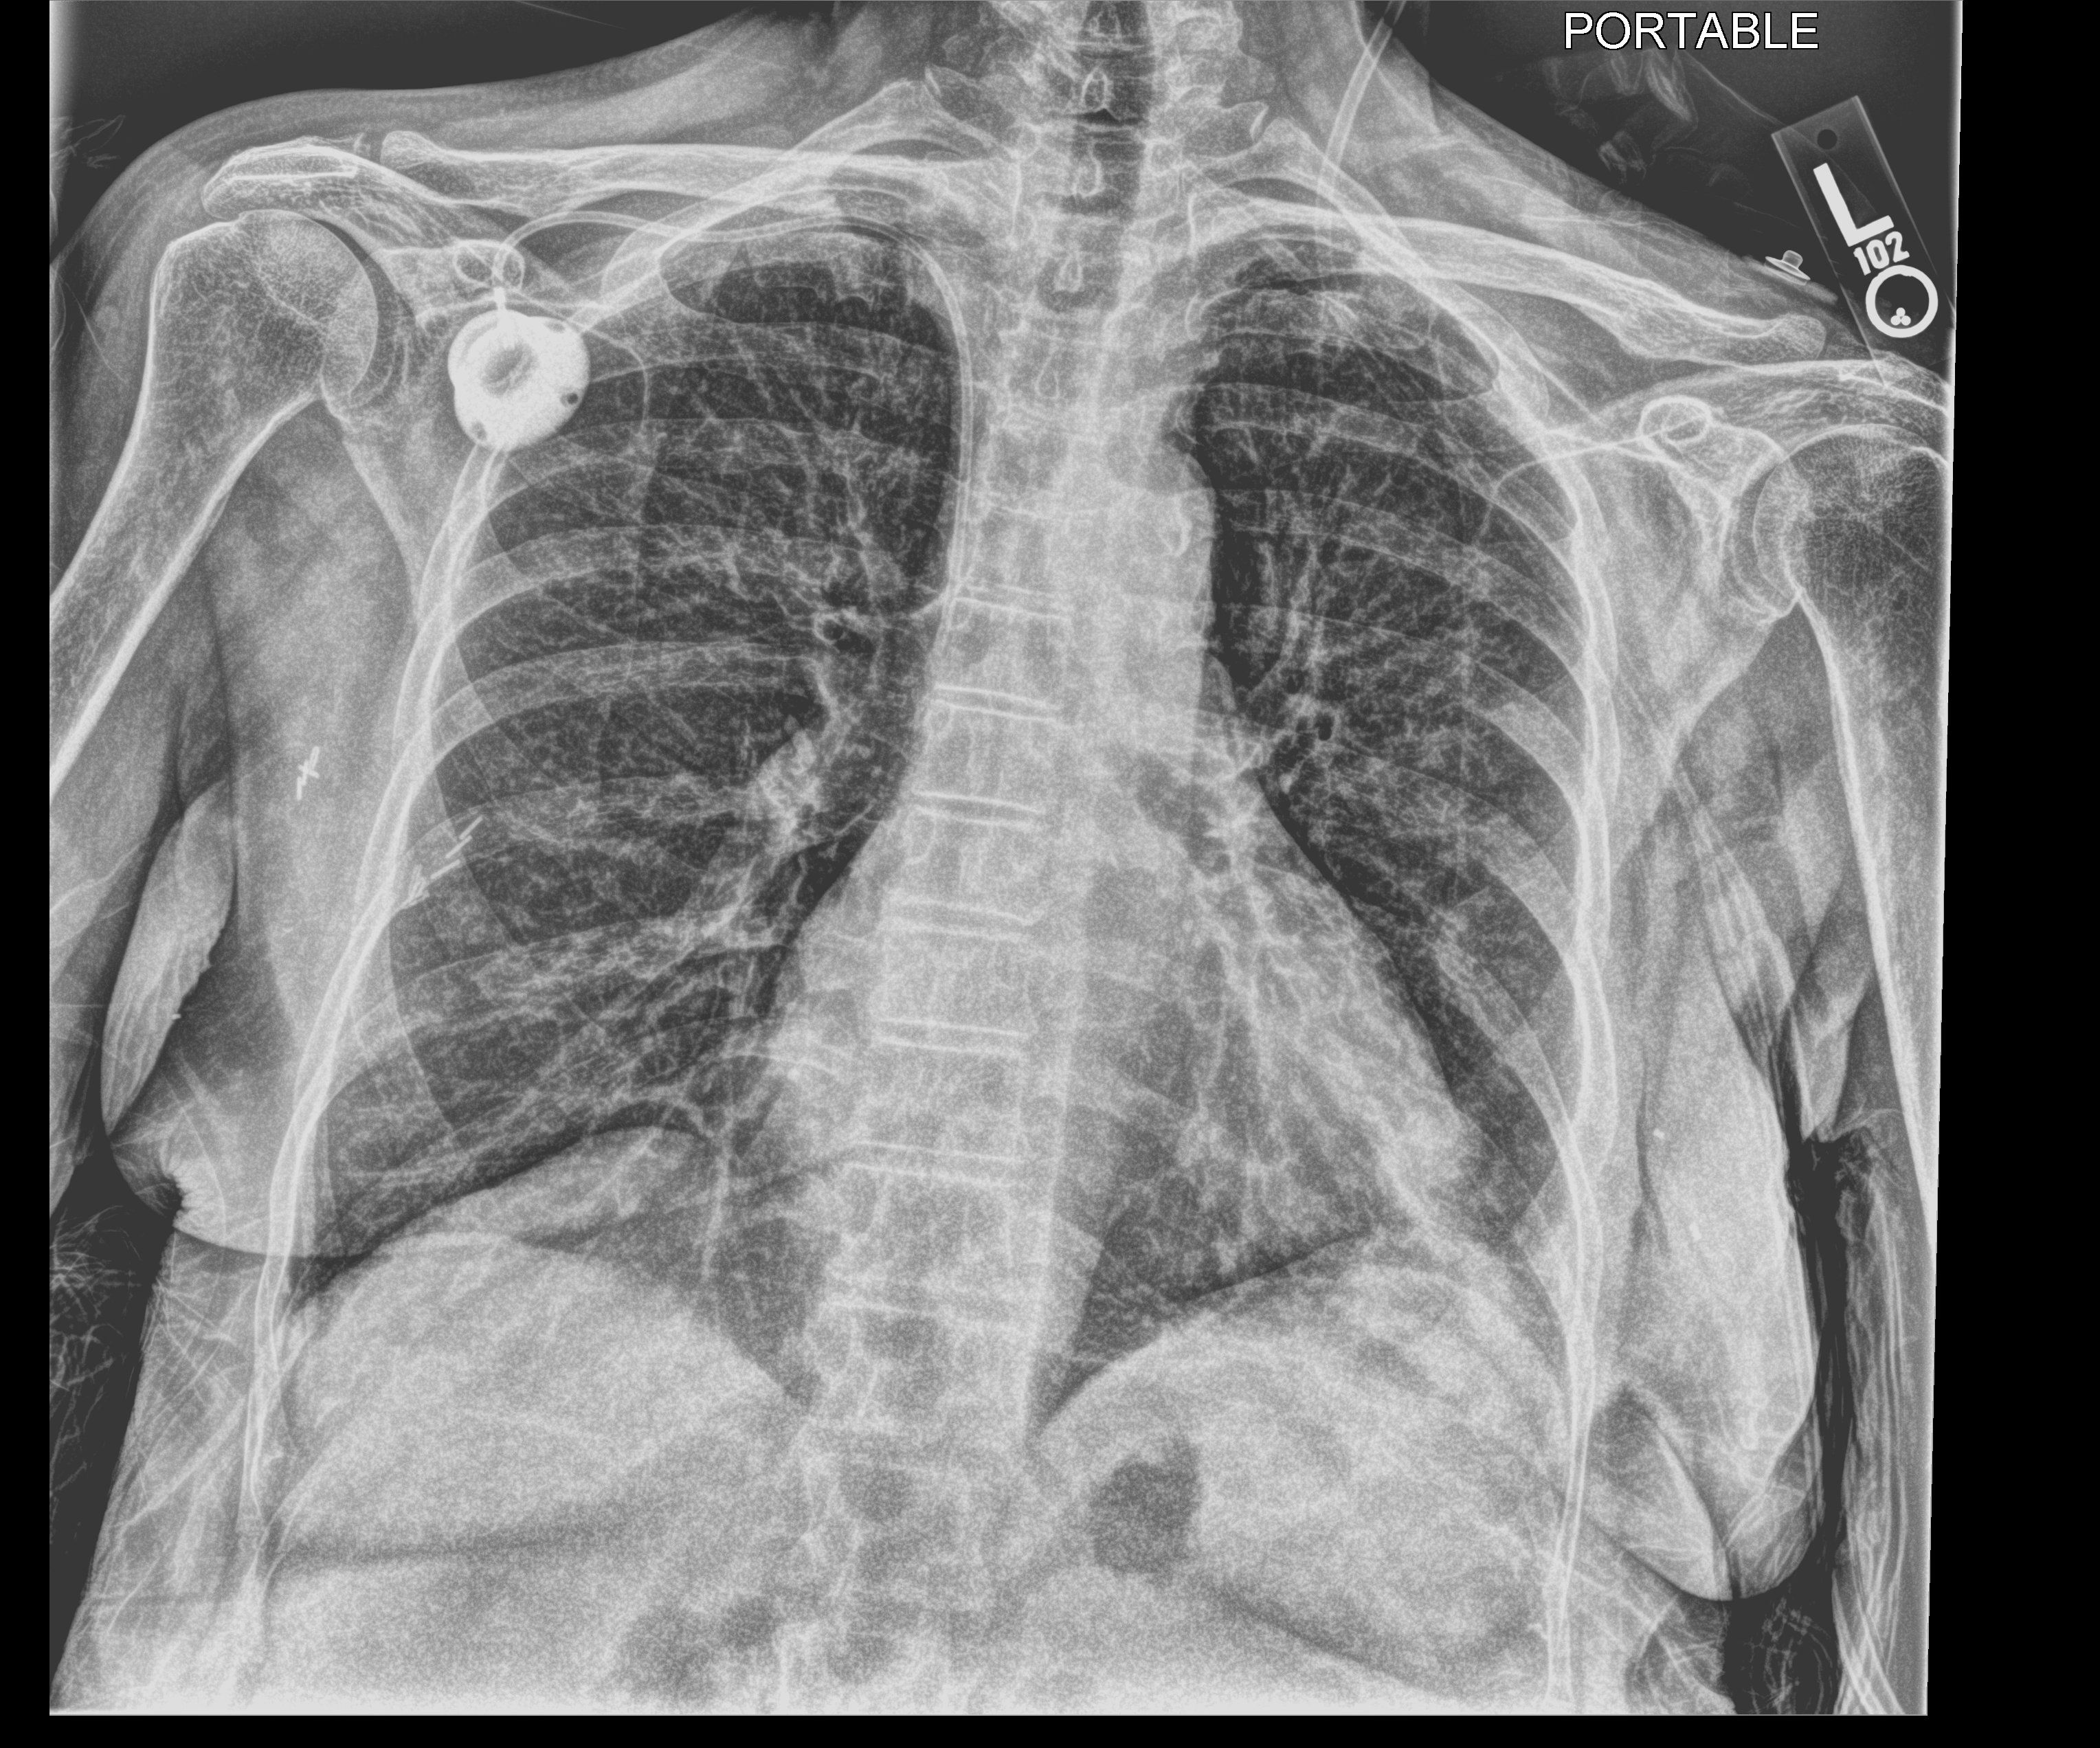
Bedside chest radiograph (computed radiography). Female patient hospitalised with COVID-19, age 60–74 years.
From the hospital-stay record, not from the radiograph (when in the stay this image was taken is not recorded): COPD (admission record): no; mechanically ventilated during this hospital stay: yes.